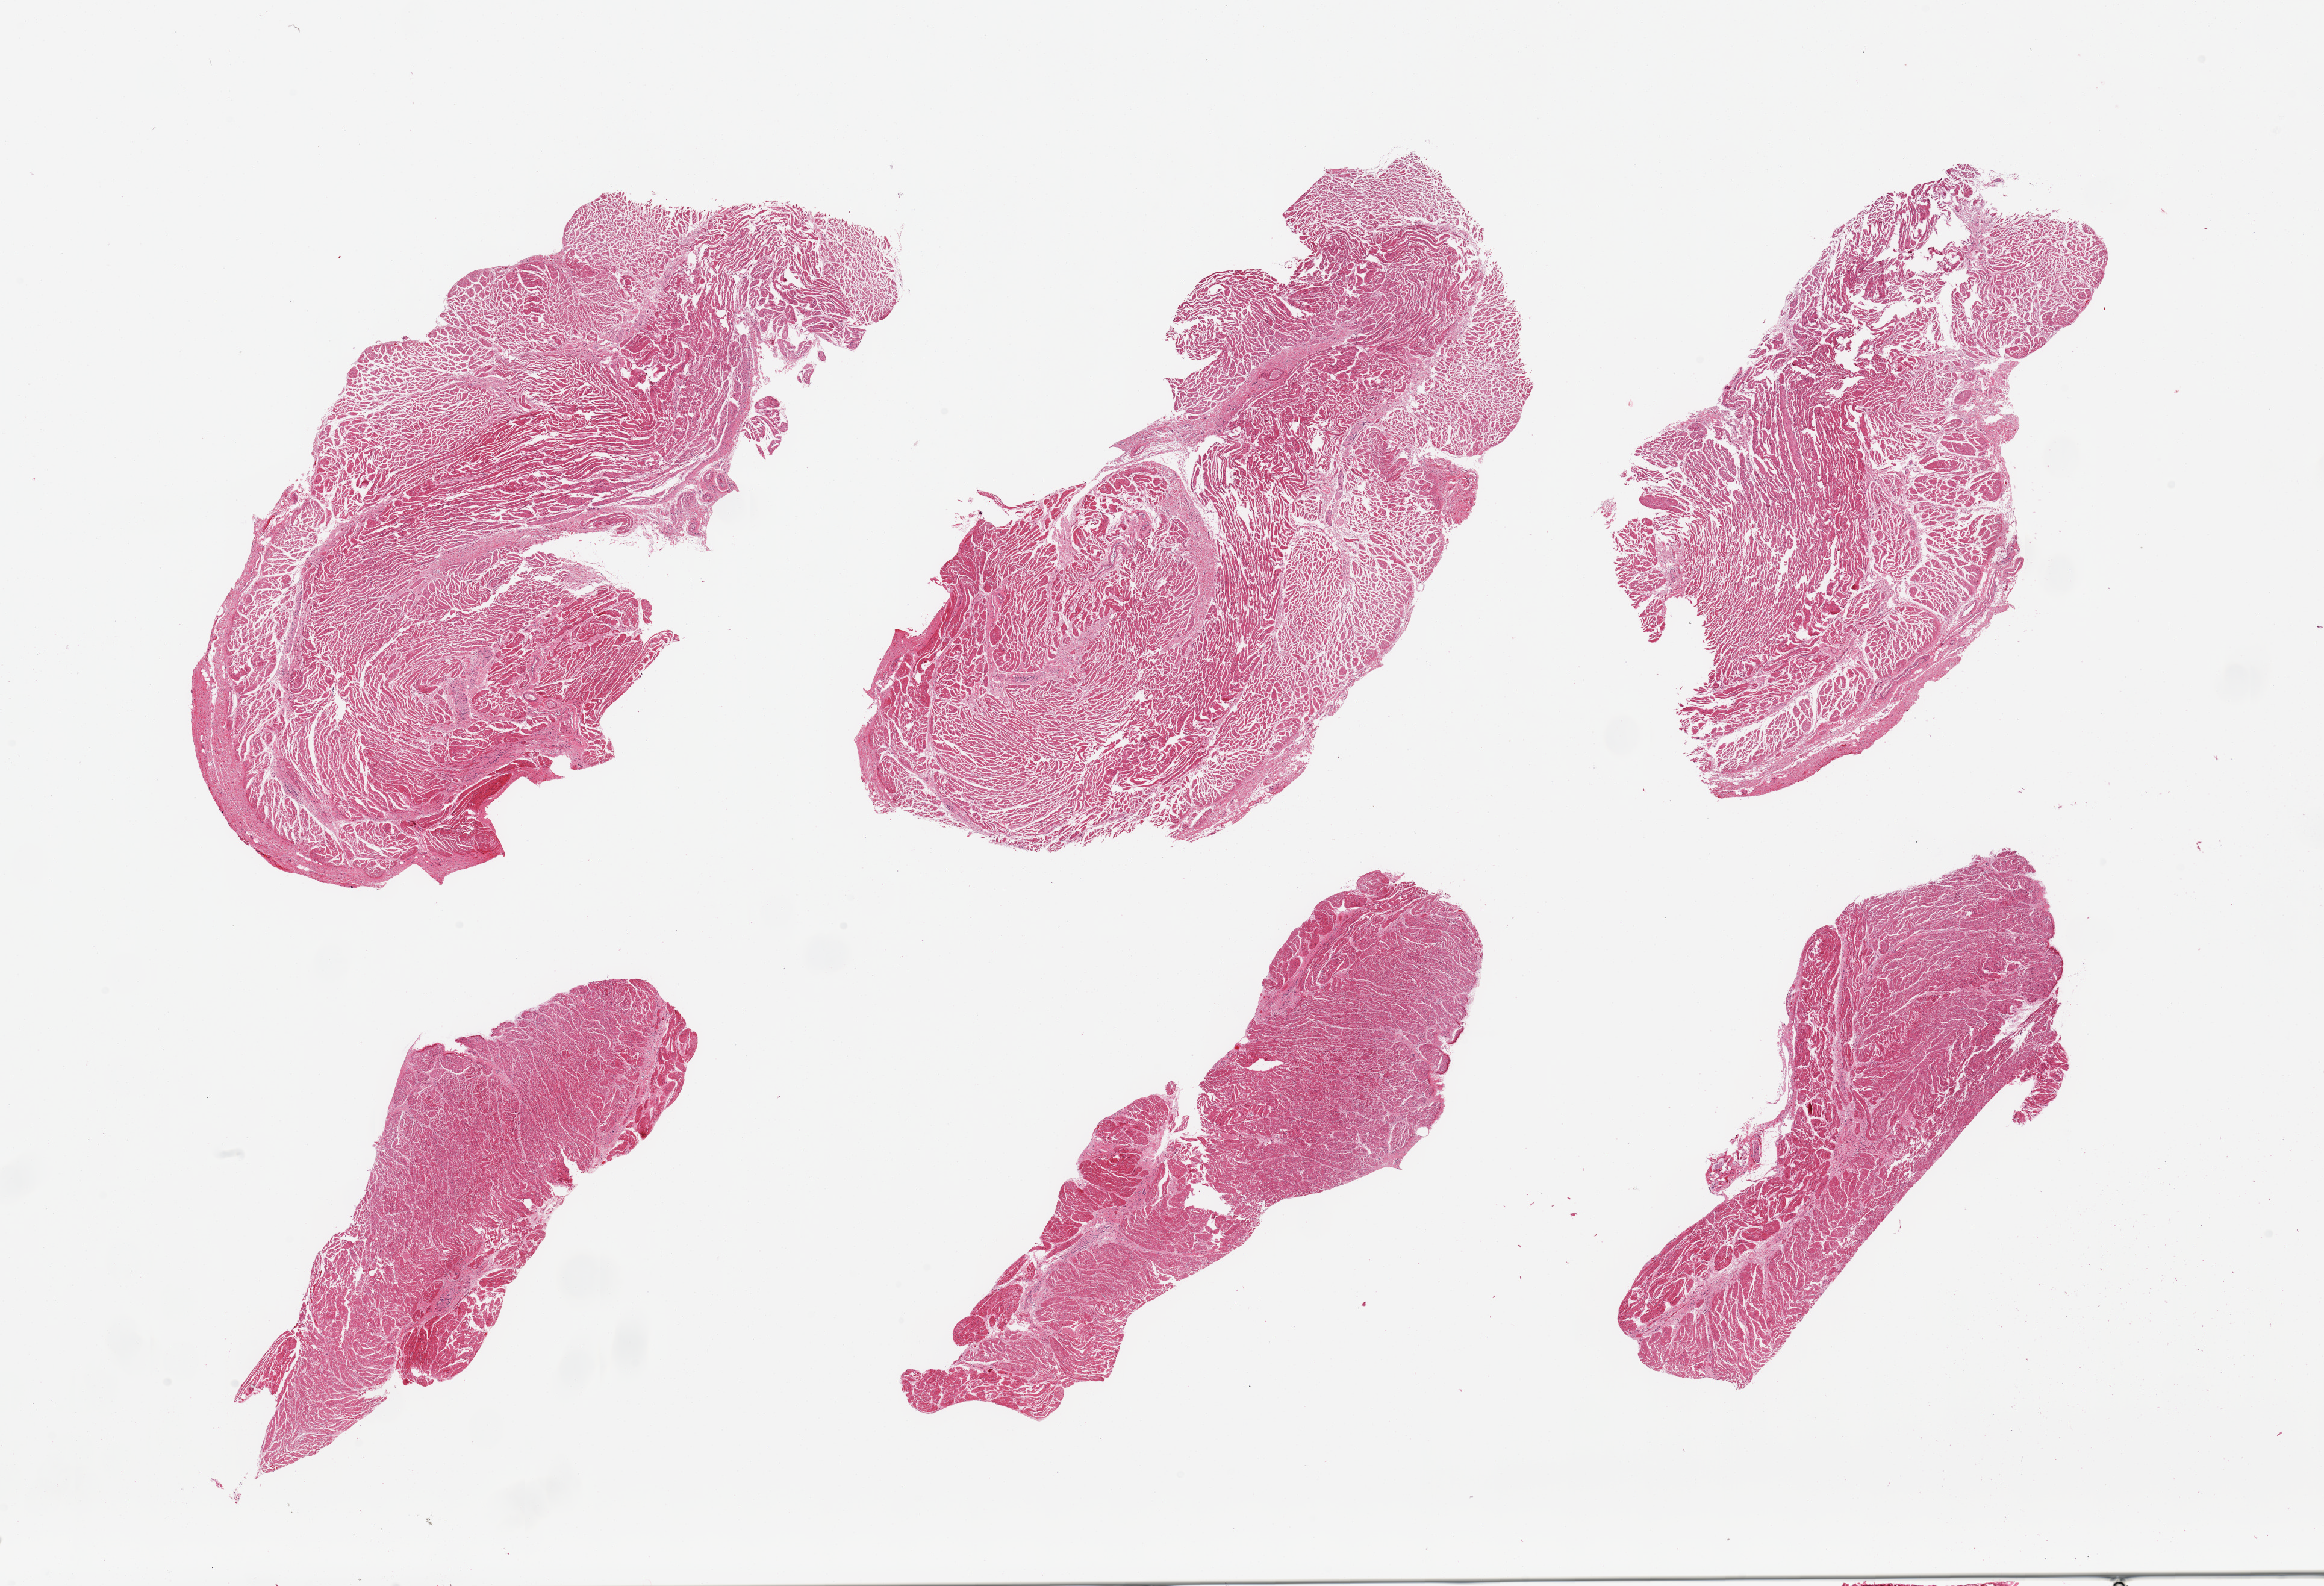
Hematoxylin and eosin (H&E) whole-slide image, brightfield, shown as a low-resolution overview of the whole scanned area (about 30.5 x 20.8 mm). PAXgene-fixed paraffin-embedded (PFPE) section. Section of gastroesophageal junction (target tissue). Tissue donor sample. Male donor.
Review note (as recorded): 6 pieces; well dissected muscularis.